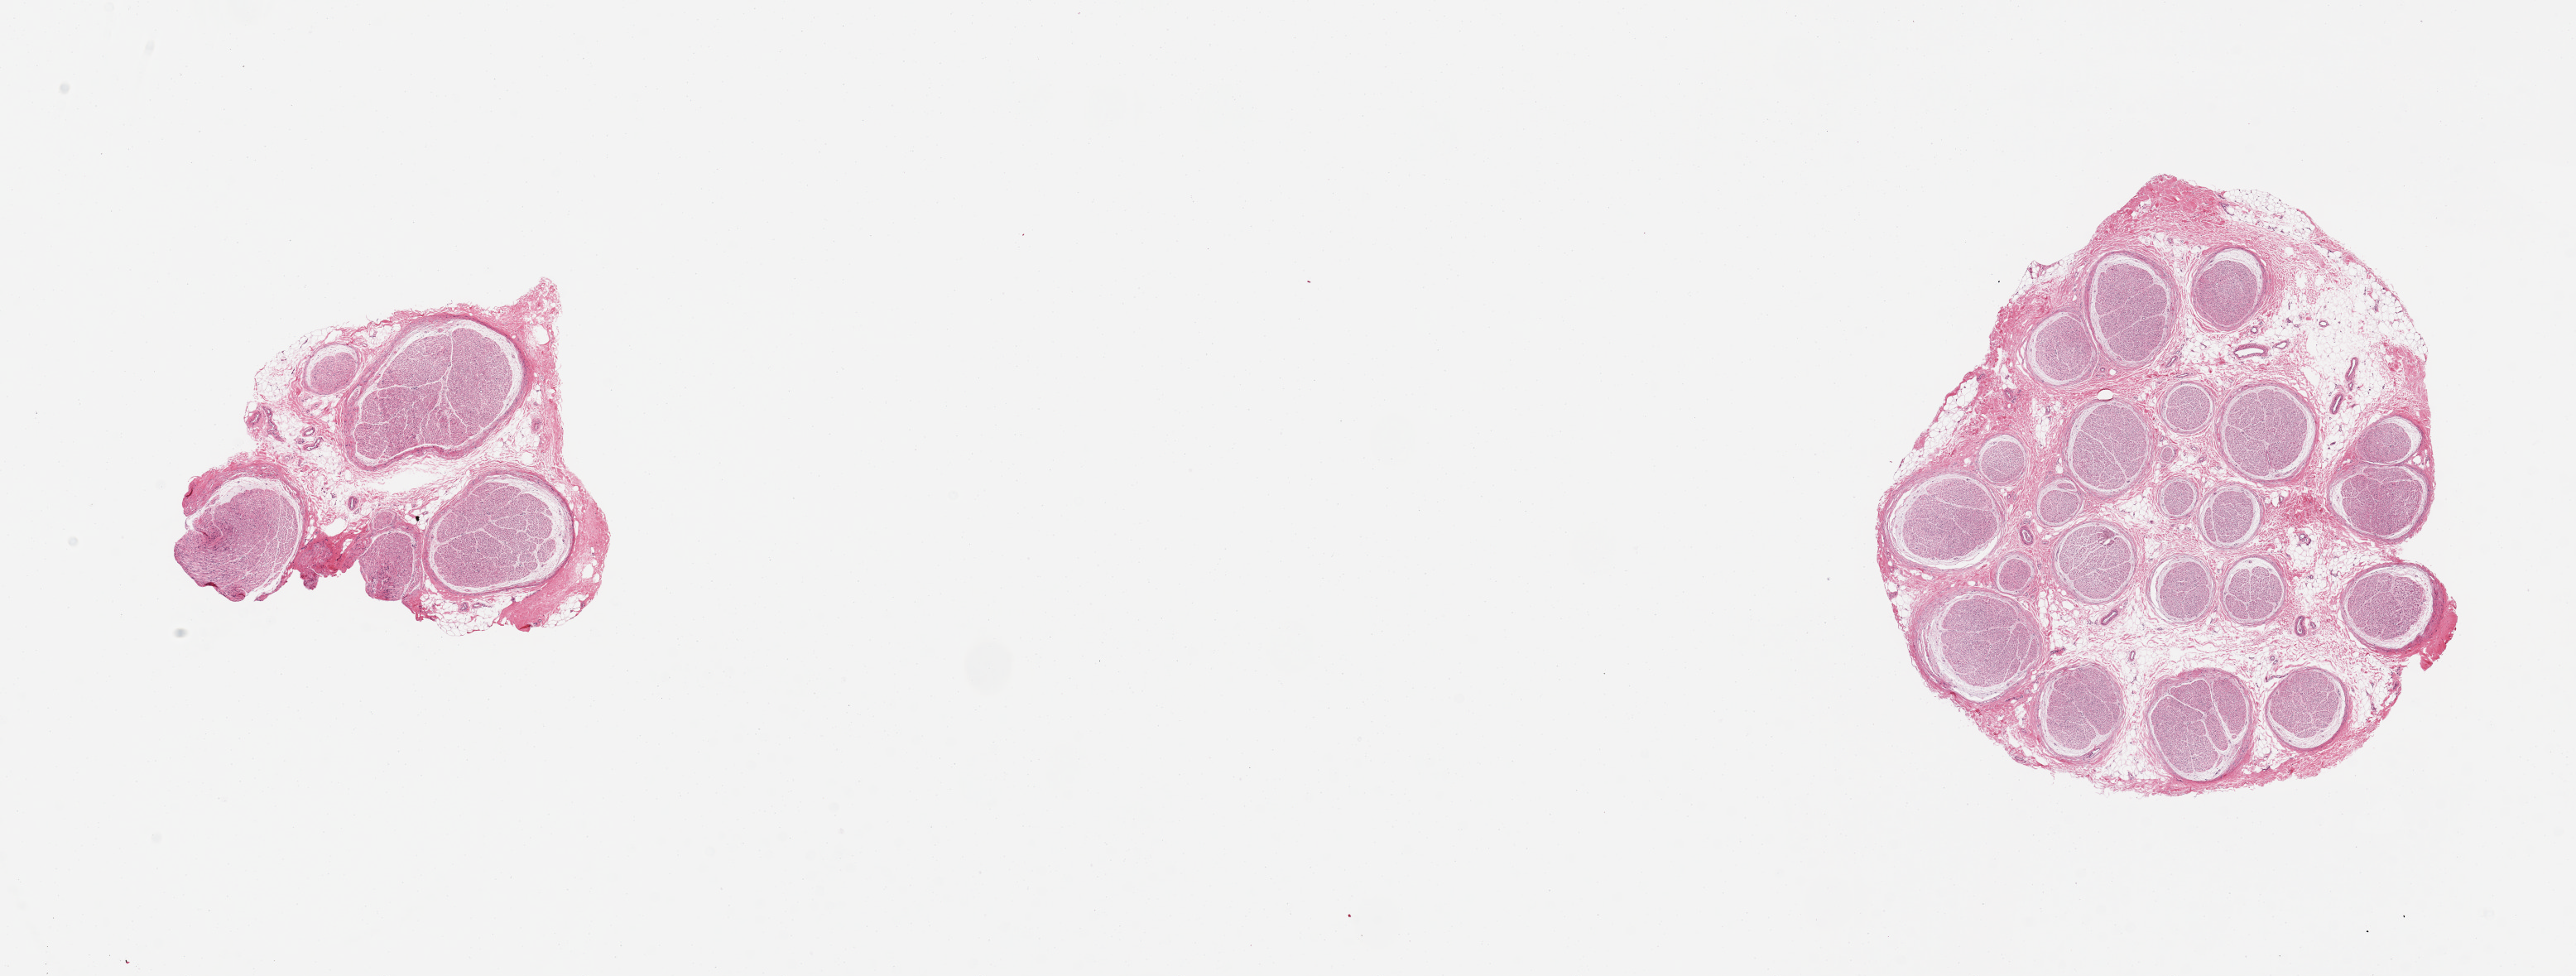
Digitized hematoxylin and eosin (H&E)-stained section, brightfield, a low-resolution overview of the entire scanned area, about 24.6 x 9.3 mm, PAXgene-fixed paraffin-embedded (PFPE) section, section of tibial nerve (target tissue), tissue donor sample. Donor sex: male.
• pathologist's review note for this sample: 2 pieces. 4x4 & 6x5mm; well trimmed, but with 20% internal fibroadipose